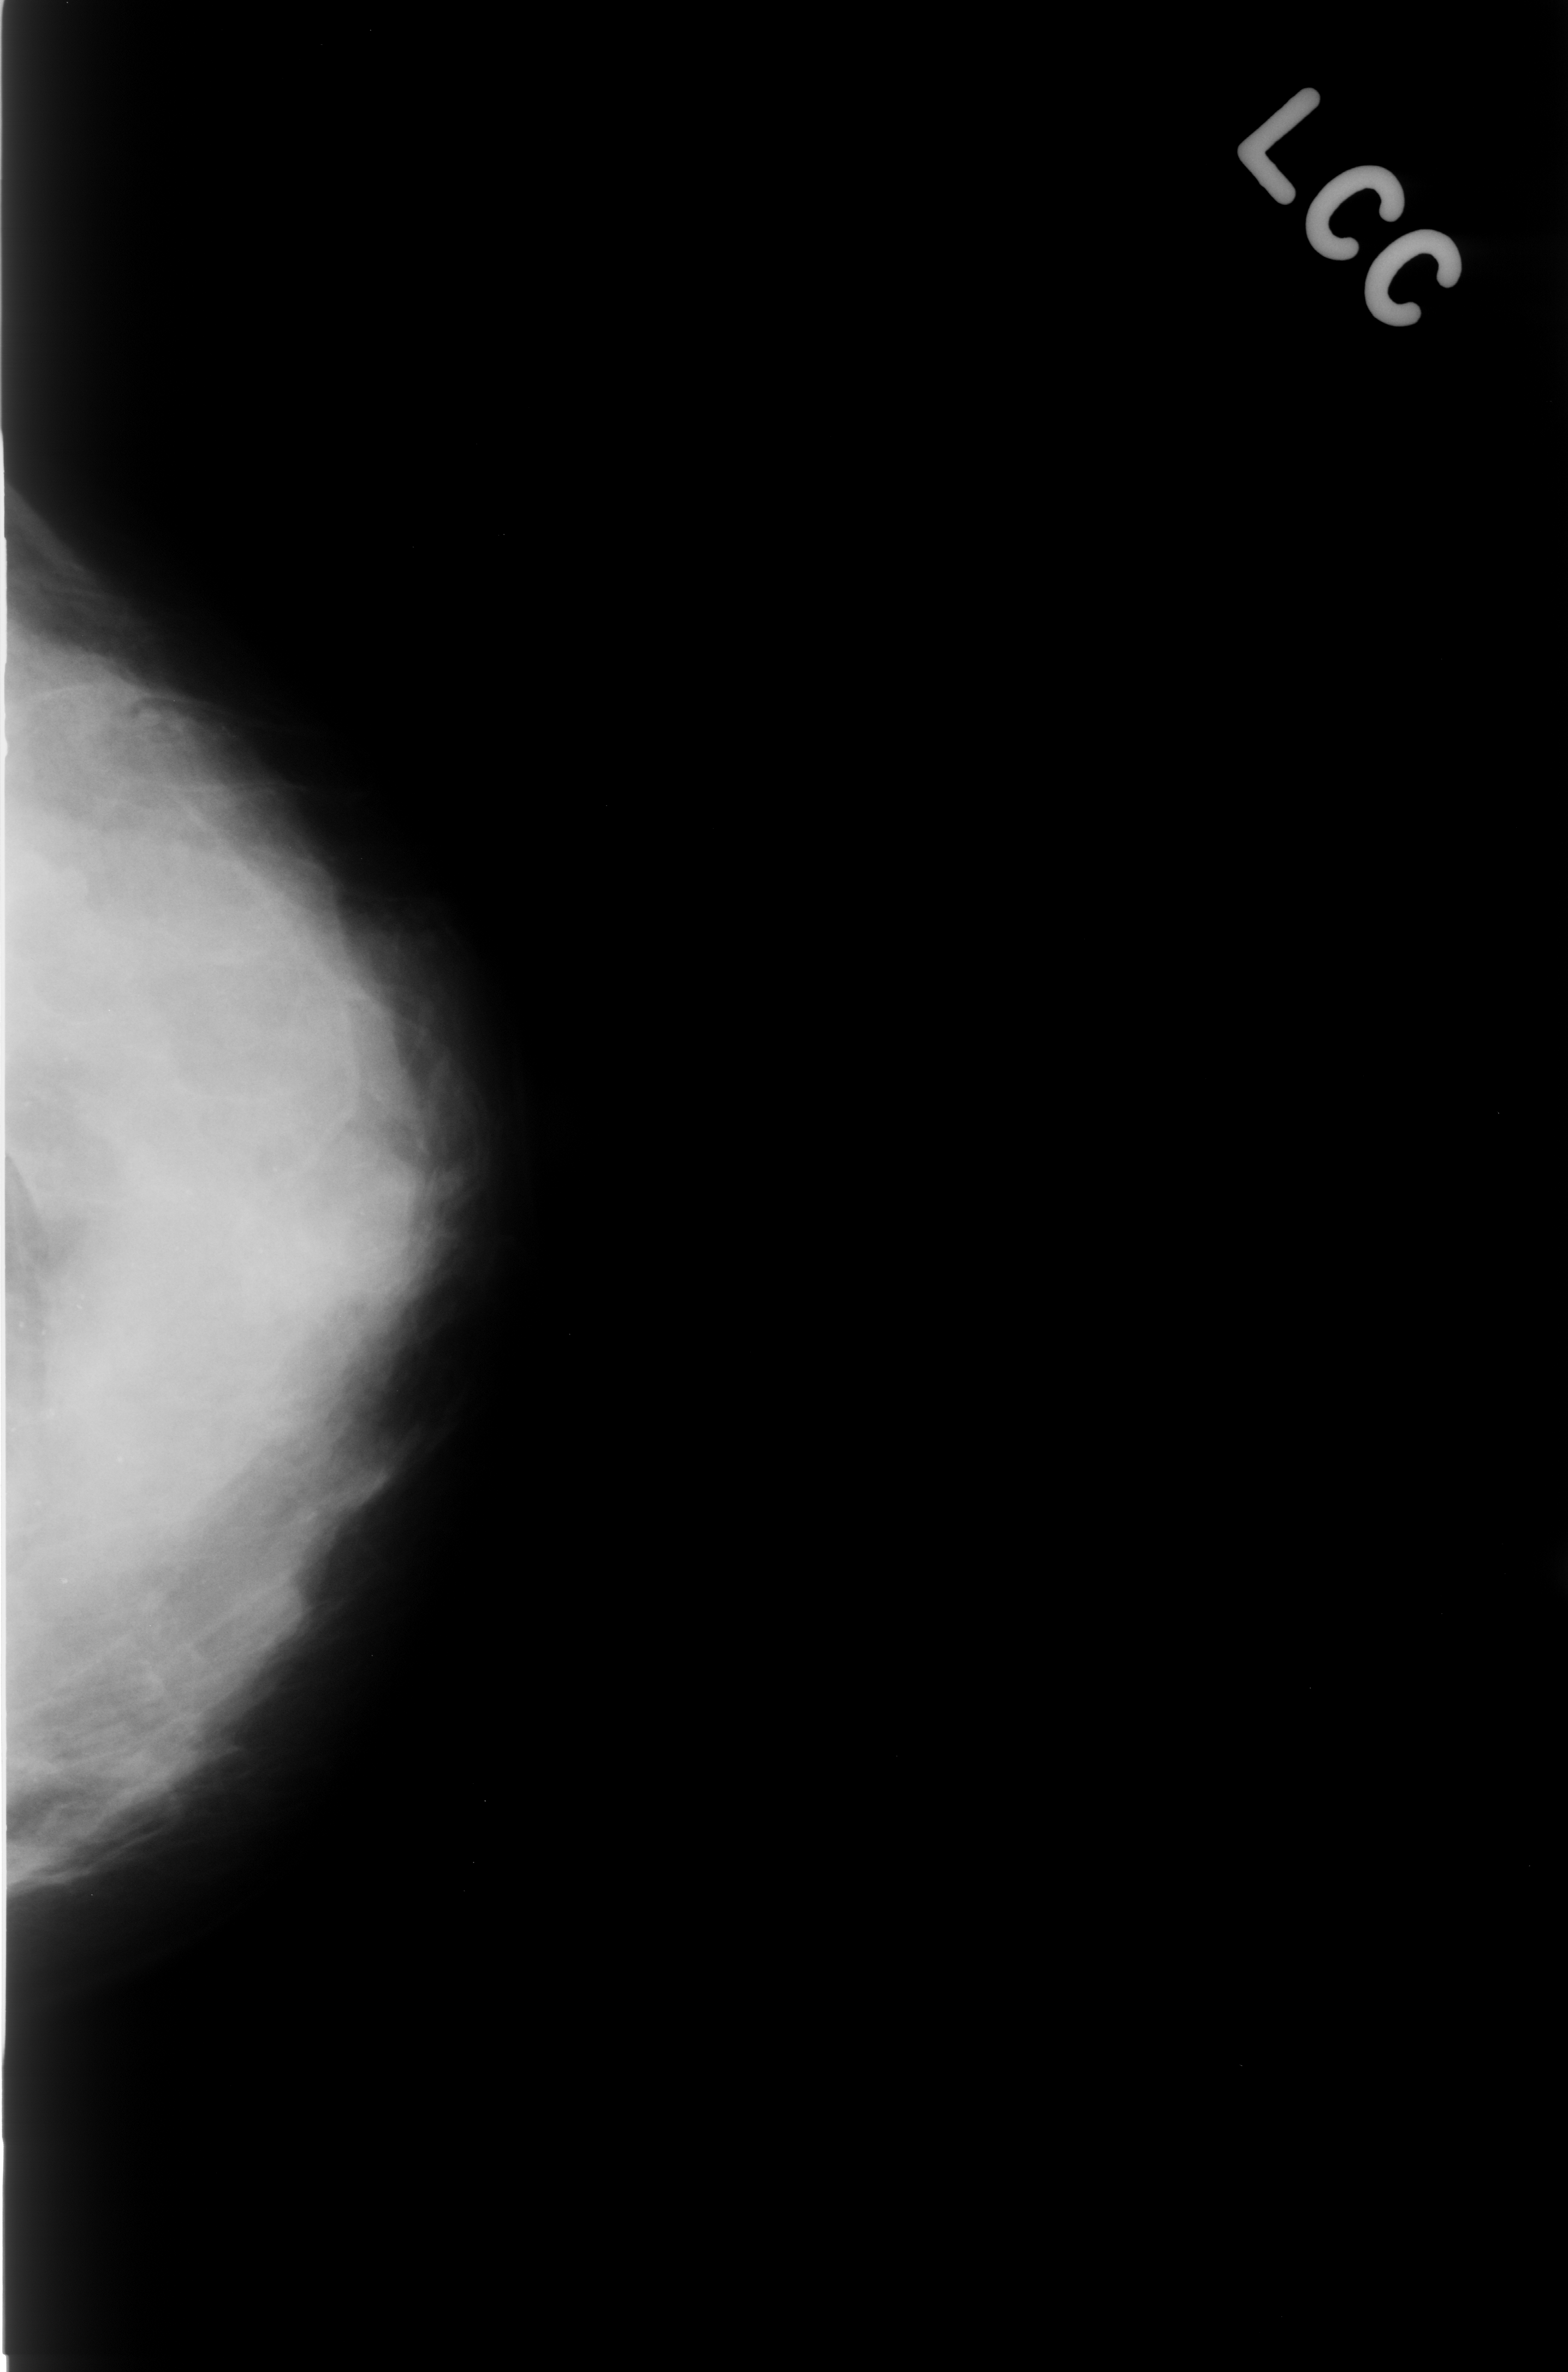
Scanned film-screen mammogram; left breast; CC view; breast composition: extremely dense (BI-RADS density category 4 of 4); 1568 × 2372 image matrix.
Expert-marked regions of interest on this image (one box per marked abnormality):
- calcifications, morphology punctate, distribution diffusely scattered; BI-RADS assessment category 2; subtlety rating 4 on a 1 (subtle) to 5 (obvious) scale; pathology (as recorded): benign: bounding box (x1, y1, x2, y2) in pixels: (0, 821, 451, 1814)